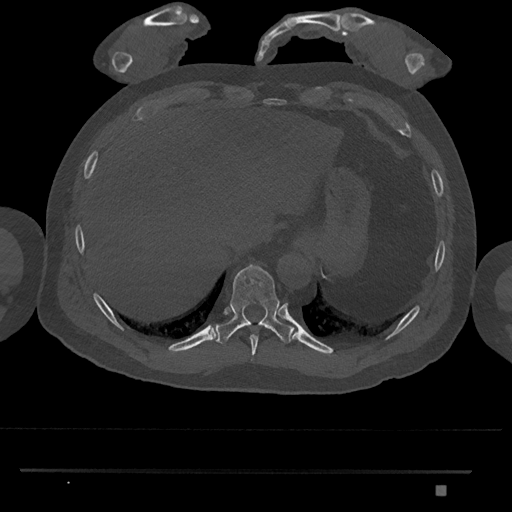
CT including the spine, one axial slice. Slice 1015 of 1134 in the series (ordered by position). Reconstruction kernel Br40s/3. 120 kVp. Bone window (W 1800 / L 400 HU). 0.5 mm slice thickness. 512 × 512 image matrix, field of view 429 × 429 mm. Male patient, age 65 years. From the clinical record (not read from this slice): primary cancer: prostate.
Structures marked on this image (semi-automatic segmentation, software-assisted and operator-edited):
- T10 vertebra: bounding box (x1, y1, x2, y2) in pixels: (214, 264, 292, 345)
- T9 vertebra: (250, 335, 259, 362)